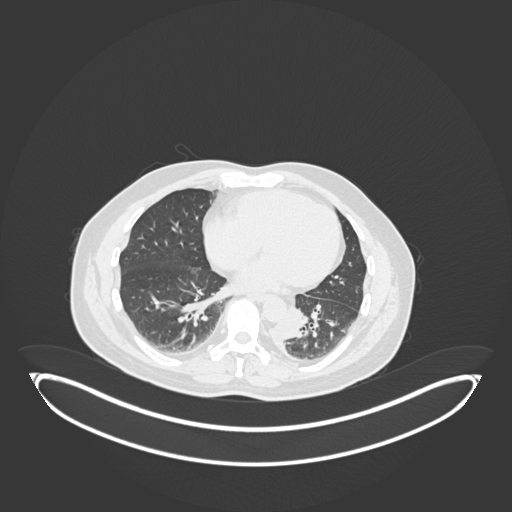
Chest CT, one axial slice; position 66 of 258 along the scan axis; reconstruction kernel B30f; 120 kVp; lung window (W 1500 / L -600 HU); 1 mm slice thickness; 512 × 512 image matrix. Male patient, age 54 years. From the clinical record (not read from this slice): clinical TNM (as recorded): T3 N0 M0.
Annotated regions visible in this slice (rectangle marked by the reading radiologist):
- lung tumour (recorded histology: squamous cell carcinoma): box from (x=273, y=307) to (x=311, y=348) px